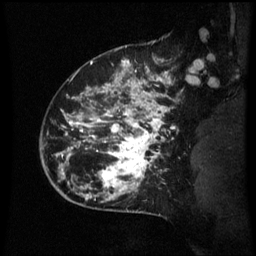
Breast MRI (dynamic contrast-enhanced), one sagittal slice. Dynamic contrast-enhanced series, image 2 of 3 at this slice position (ordered by acquisition). 1.5 T. TE 4.2 ms, TR 8.9 ms. 2.1 mm slice thickness. 256 × 256 image matrix. Patient: female, 42 years. Case-level facts recorded for this patient, not image findings: setting: breast cancer imaged before/during neoadjuvant chemotherapy; receptor status: HER2-positive.
Structures marked on this image (semi-automatically segmented with operator editing):
- analysis volume of interest (the breast-tissue region the enhancement analysis was run in; not a lesion): box from (x=66, y=82) to (x=173, y=193) px
- tumour enhancement mask (voxels above the 70 % enhancement threshold inside the analysis volume of interest): (x=68, y=82)–(x=169, y=191)